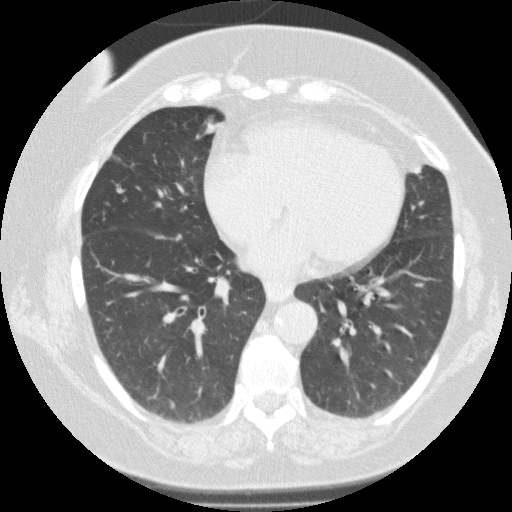
Low-dose screening chest CT, one axial slice; slice 59 of 146 in the series (ordered by position); reconstruction kernel FC01; 120 kVp; lung window (W 1500 / L -600 HU); 2 mm slice thickness; 512 × 512 image matrix, field of view 330 × 330 mm.
Structures marked on this image (expert manual segmentation):
- lesion 1 (nodule, lower lobe of right lung): bounding box <164,399,177,412> (left, top, right, bottom; pixels)